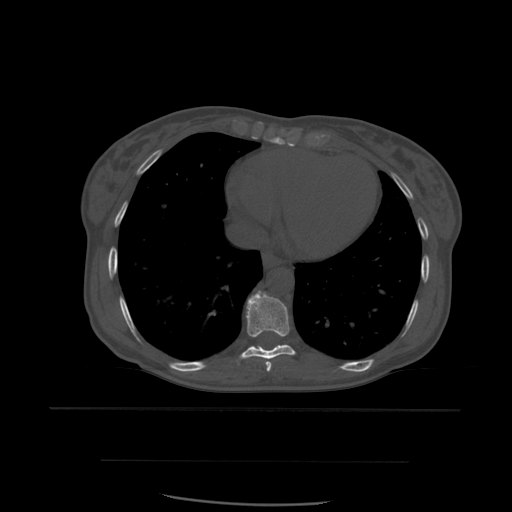
CT including the spine, one axial slice. Slice 336 of 574 in the series (ordered by position). Bone window (W 1800 / L 400 HU). 512 × 512 image matrix, field of view 392 × 392 mm. Patient age 48 years. From the clinical record (not read from this slice): primary cancer: lung; vertebrae with lytic lesions (as recorded): T11.
Annotated regions visible in this slice (semi-automatically segmented with operator editing):
- T8 vertebra: bounding box <265,361,272,372> (left, top, right, bottom; pixels)
- T9 vertebra: <240,291,296,360>